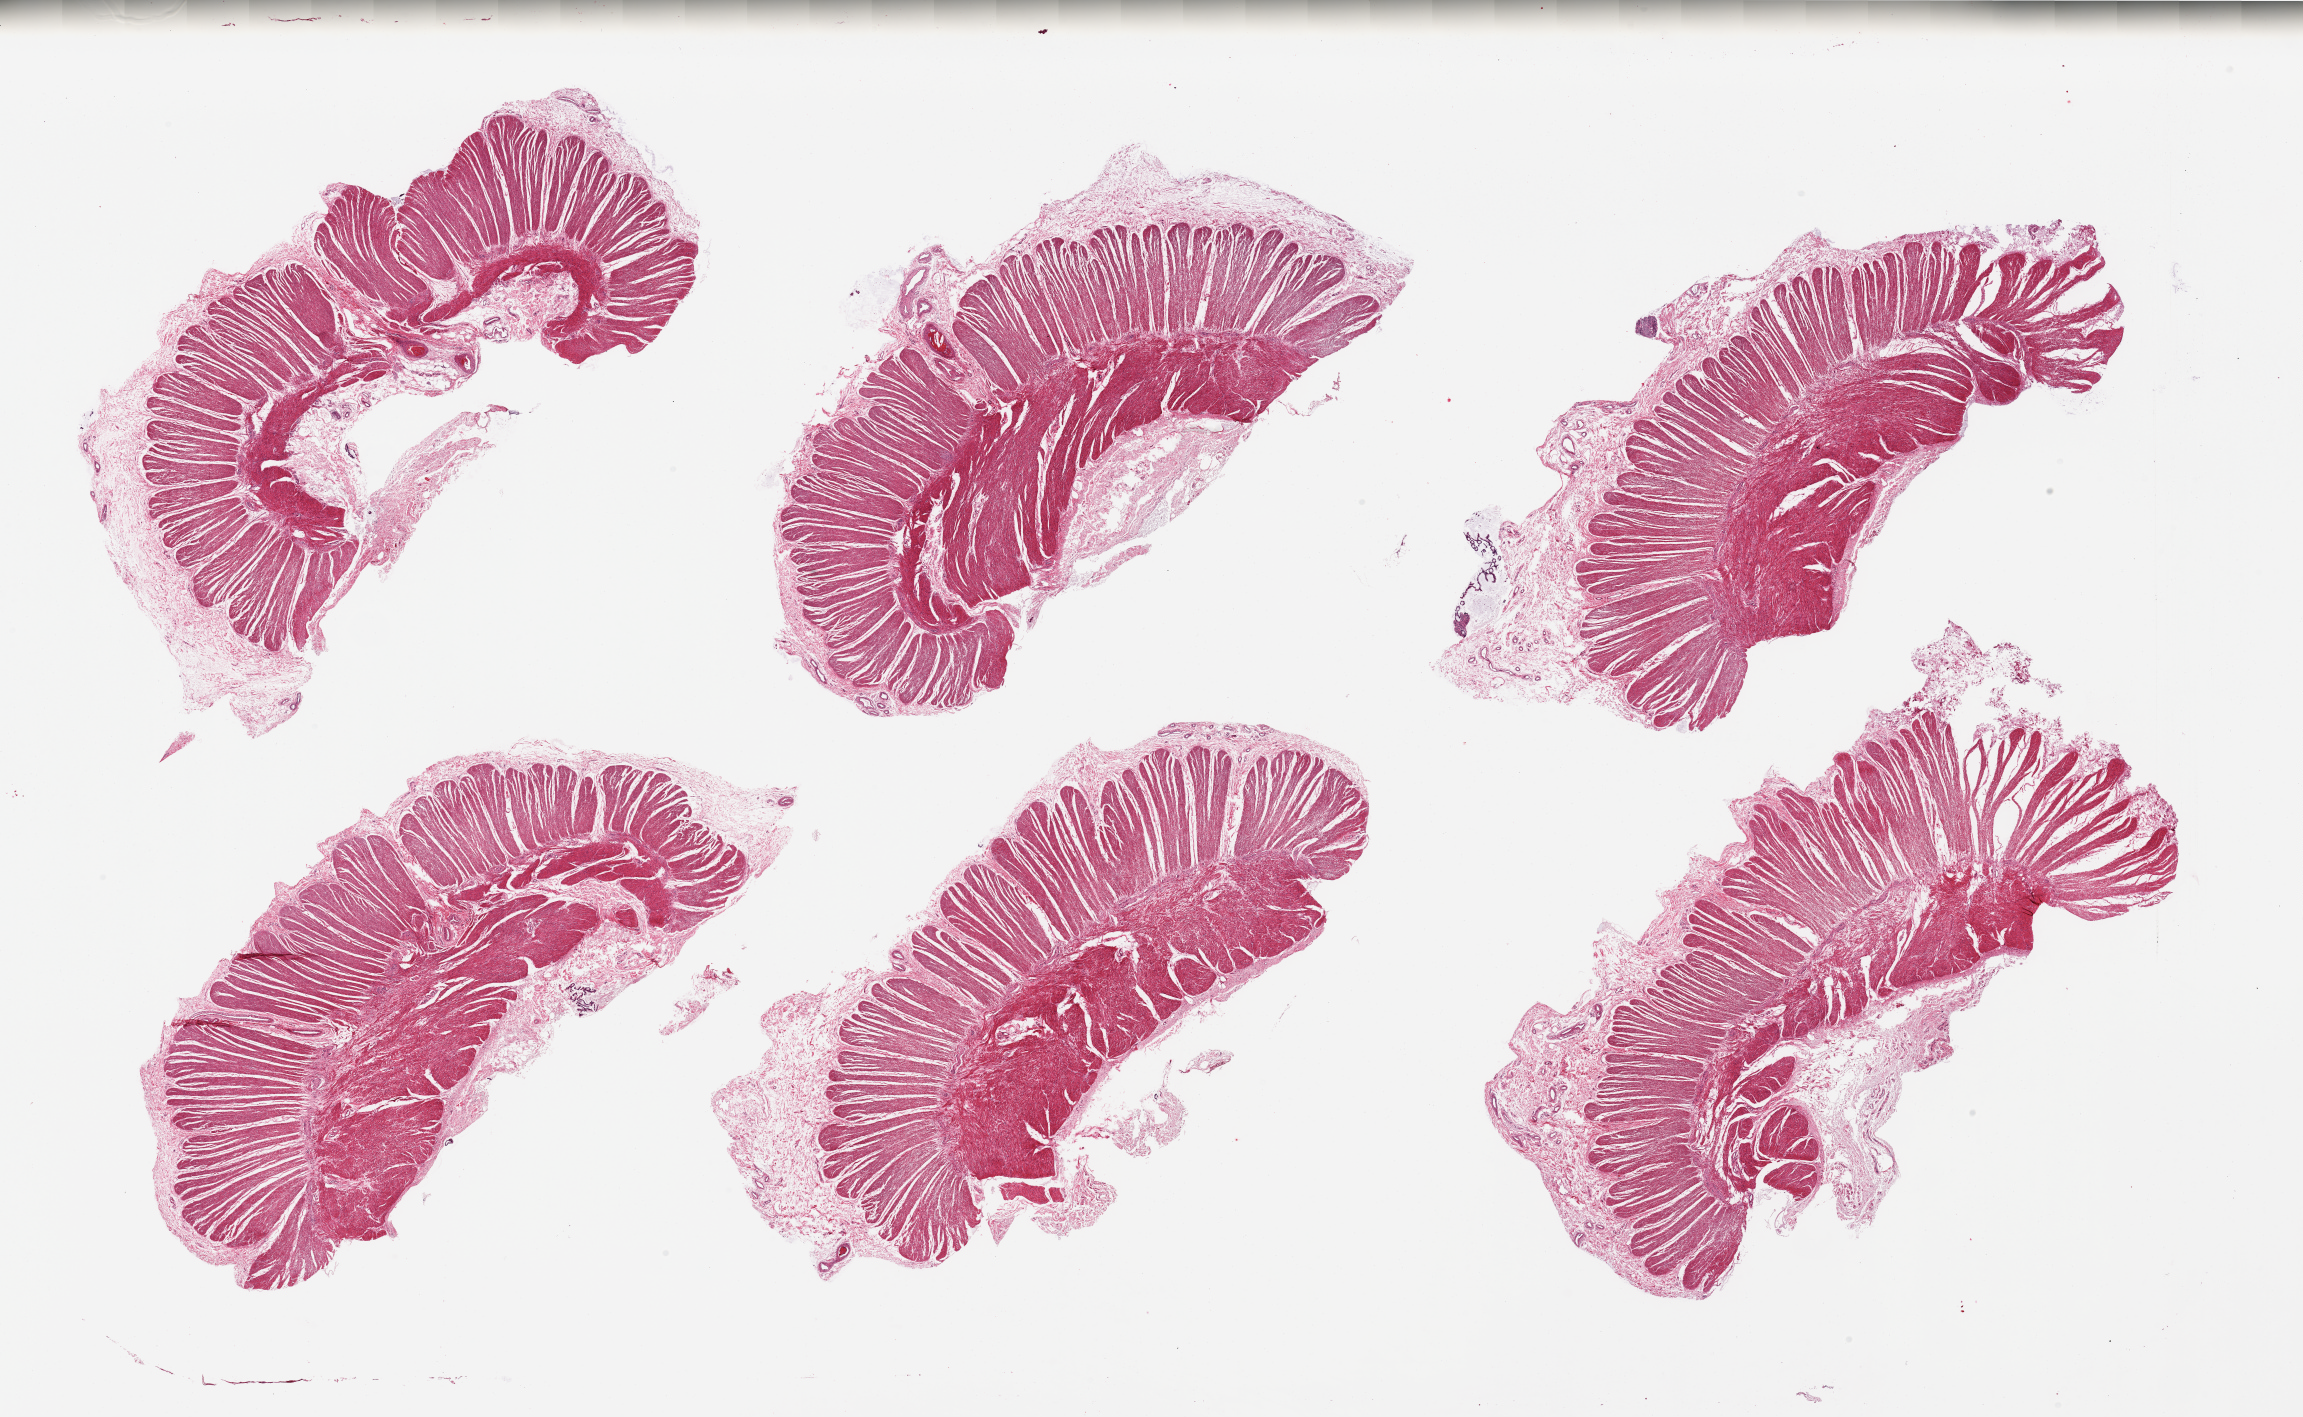
Digitized haematoxylin and eosin-stained section, shown as a low-resolution overview of the whole scanned area (about 36.4 x 22.4 mm, slide scanned at 20x), PAXgene-fixed paraffin-embedded (PFPE) section, sampled site (target tissue): sigmoid colon, tissue donor sample.
Pathologist's review note for this sample: 6 pieces, adherent fat/serosal nubbins up to ~2mm.